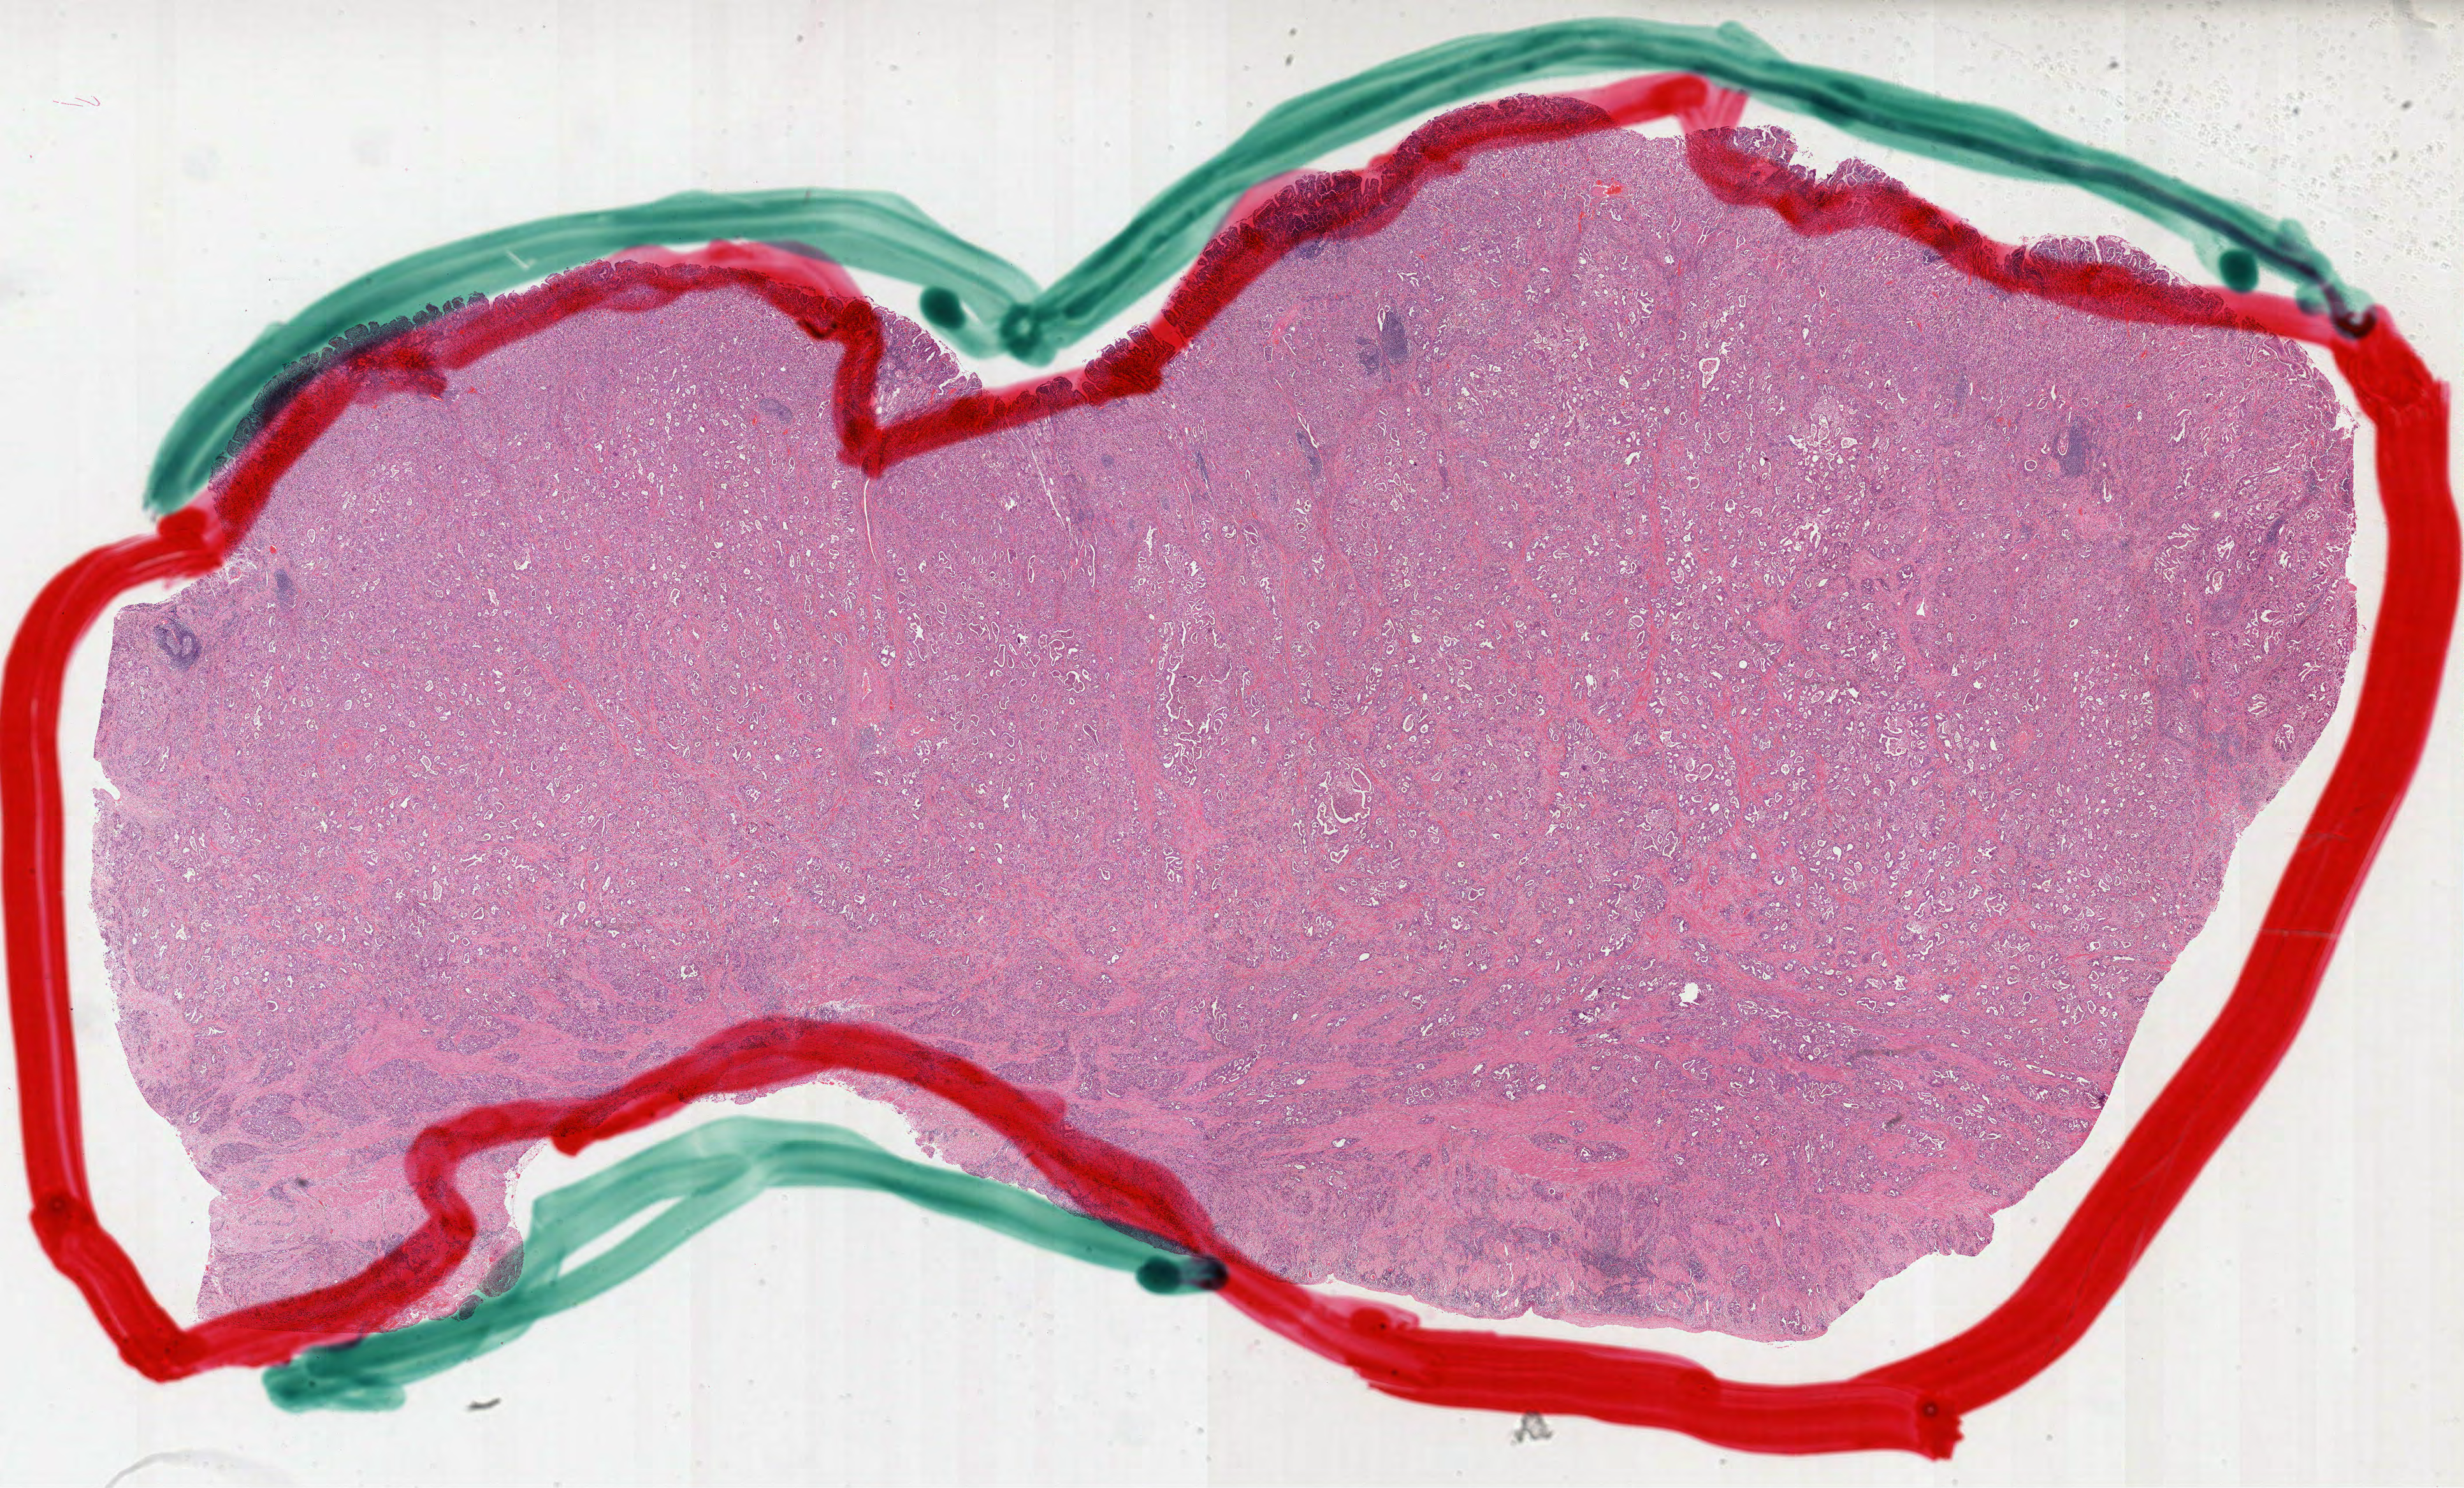
Digitized H&E-stained tissue section (whole slide) — whole scanned area (about 31.2 x 18.8 mm, acquisition: 40x scan) shown as a low-resolution overview, formalin-fixed paraffin-embedded (FFPE) diagnostic section, primary tumour sample from the stomach. Patient: female, age at initial diagnosis 58 years. Histologic grade: G3 (poorly differentiated).
AJCC pathologic stage: IIIC (7th edition). Lymph nodes positive (case pathology): 6 of 7 examined. Histologic diagnosis: Adenocarcinoma, intestinal type (body of stomach).